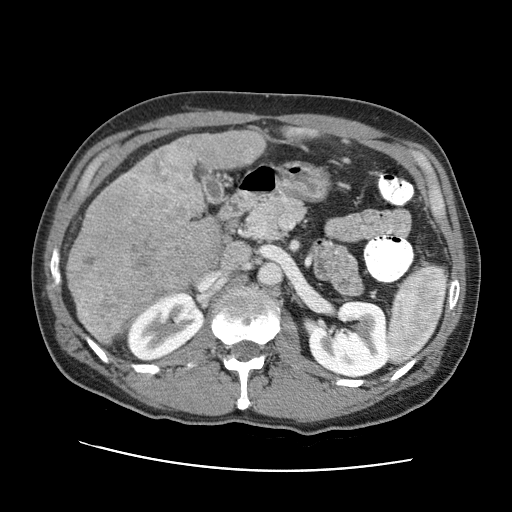
Contrast-enhanced abdominal CT (liver protocol), one axial slice. Position 34 of 95 along the scan axis. One of 2 acquisitions stored at this slice position. Soft-tissue window (W 400 / L 40 HU). 2.5 mm slice thickness. 512 × 512 image matrix, field of view 360 × 360 mm. Case-level facts recorded for this patient, not image findings: diagnosis: hepatocellular carcinoma (patient treated with transarterial chemoembolisation; whether this scan precedes or follows treatment is not stated here); TNM stage (as recorded): Stage-IVA; Child-Pugh class: A; tumour differentiation: moderately differentiated.
Annotated regions visible in this slice (semi-automatically segmented with operator editing):
- liver parenchyma outside the tumour (the mass and vessels are separate outlines, so this box may not span the whole liver): box from (x=92, y=130) to (x=264, y=311) px
- mass: (x=73, y=144)–(x=215, y=338)